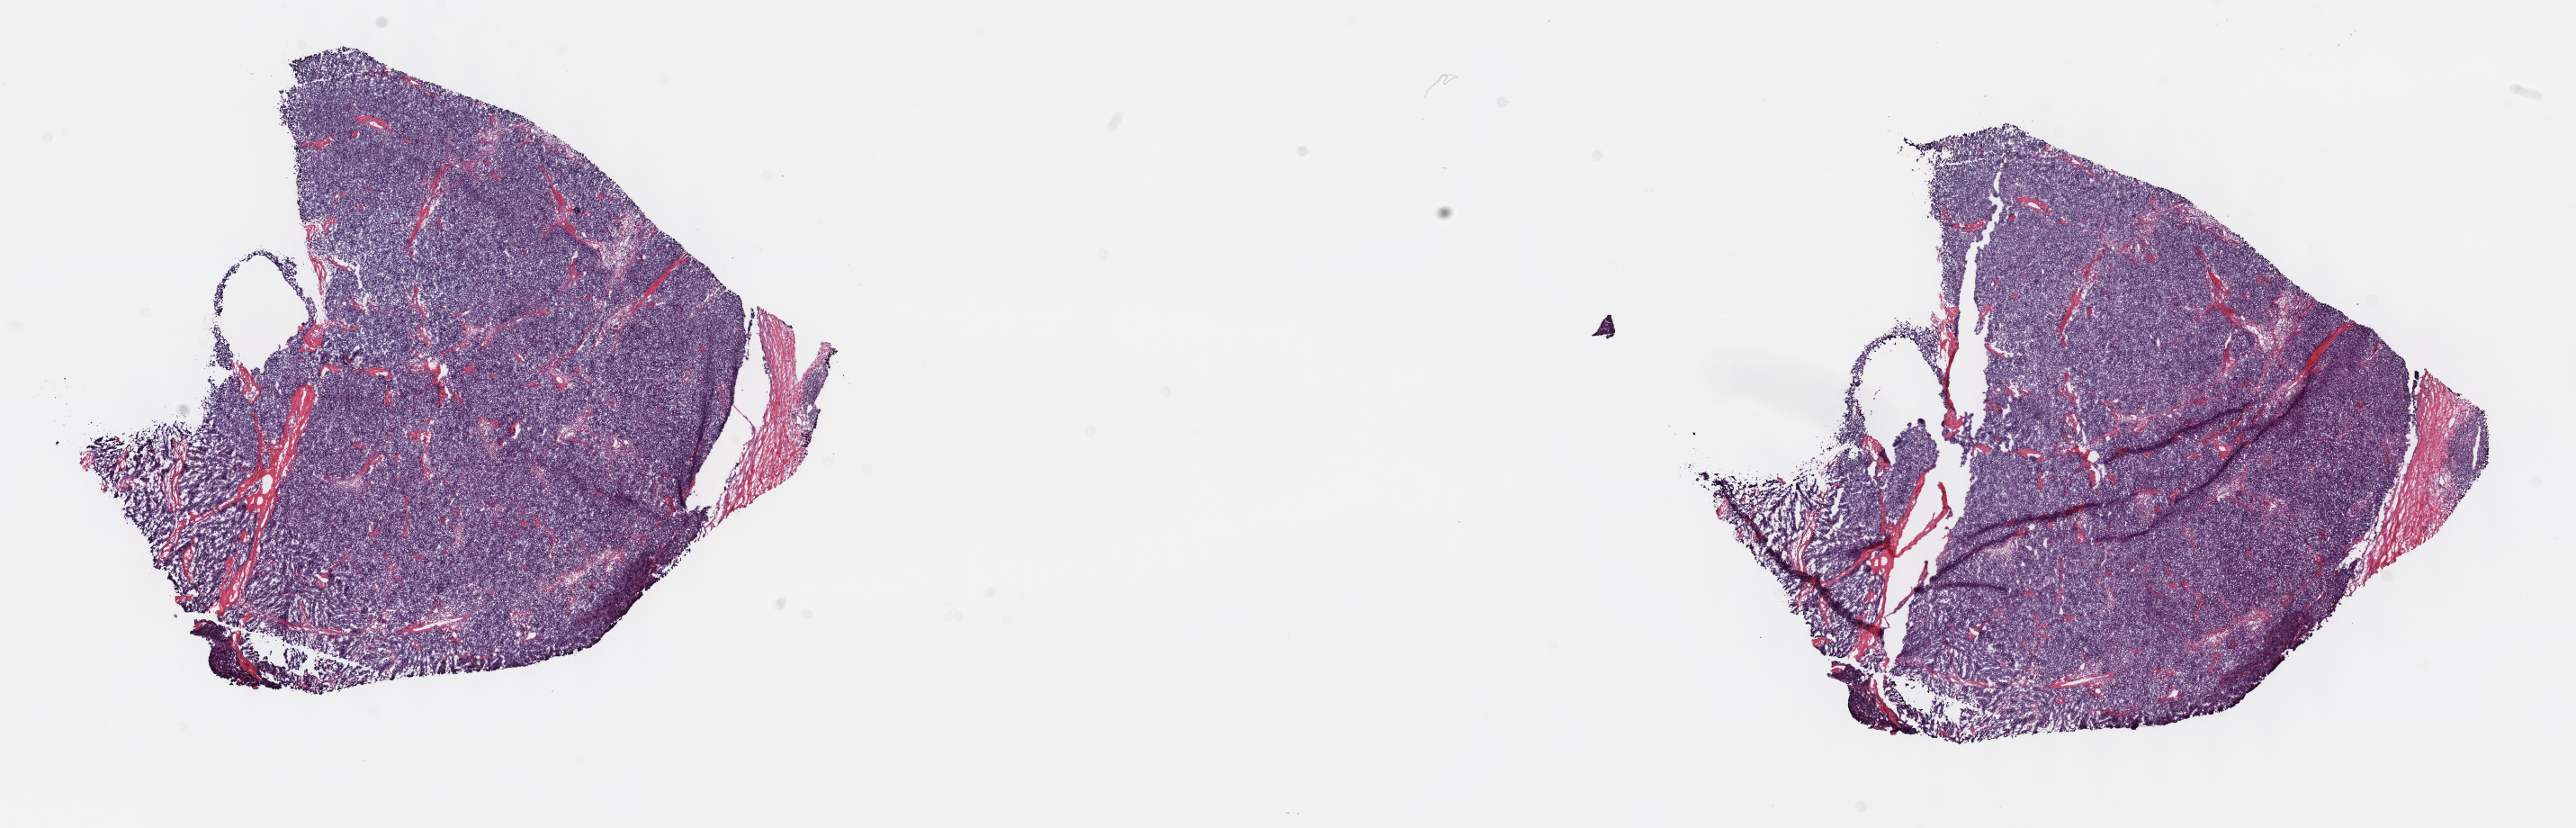
Whole-slide histology image, Hematoxylin and eosin (H&E) stained, whole scanned area (about 23.2 x 7.4 mm, slide scanned at 40x) shown as a low-resolution overview; frozen section from the top of the tissue portion; thymus, primary tumour sample. Patient: female, age at initial diagnosis 50 years. Composition of this section per pathologist review: tumour cells 100%, tumour nuclei 80%, normal cells 0%, stromal cells 0%, necrosis 0%. Infiltration values recorded for this section: lymphocyte infiltration 2%, monocyte infiltration 0%, neutrophil infiltration 0%.
* histologic diagnosis: Thymoma, type AB, malignant